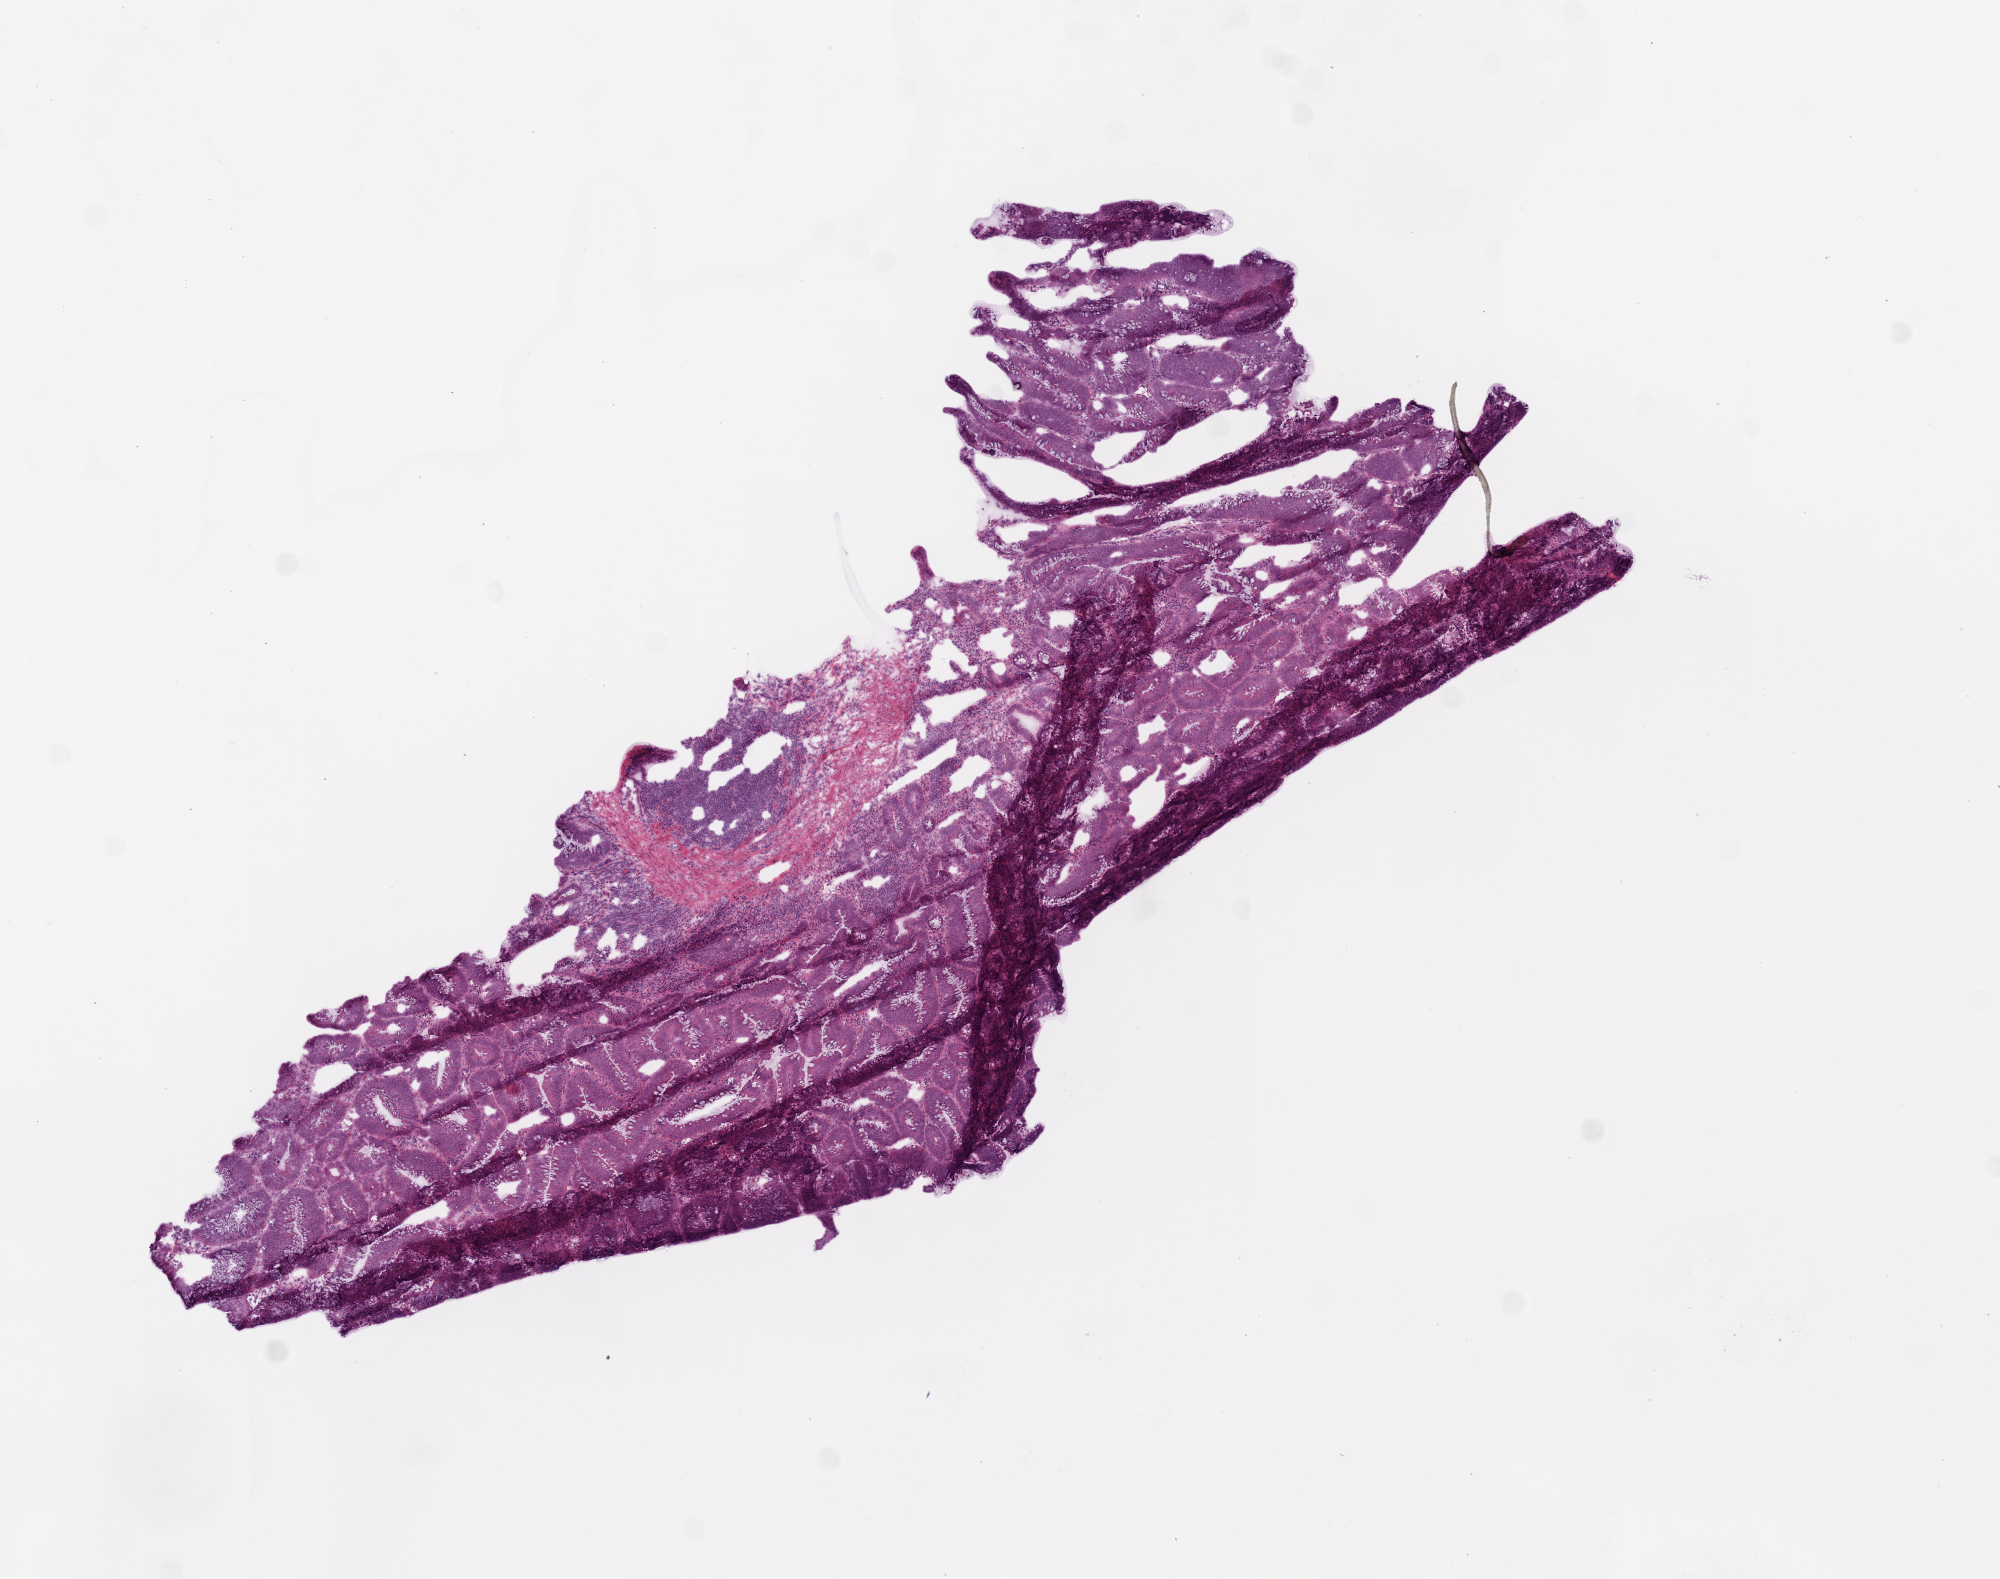
Hematoxylin and eosin (H&E) stained whole-slide image, low-resolution overview of the scanned area, about 8.0 x 6.3 mm, frozen section from the top of the tissue portion, colon, primary tumour sample. Patient: female, age at initial diagnosis 67 years.
Diagnosis: Adenocarcinoma, NOS (cecum).